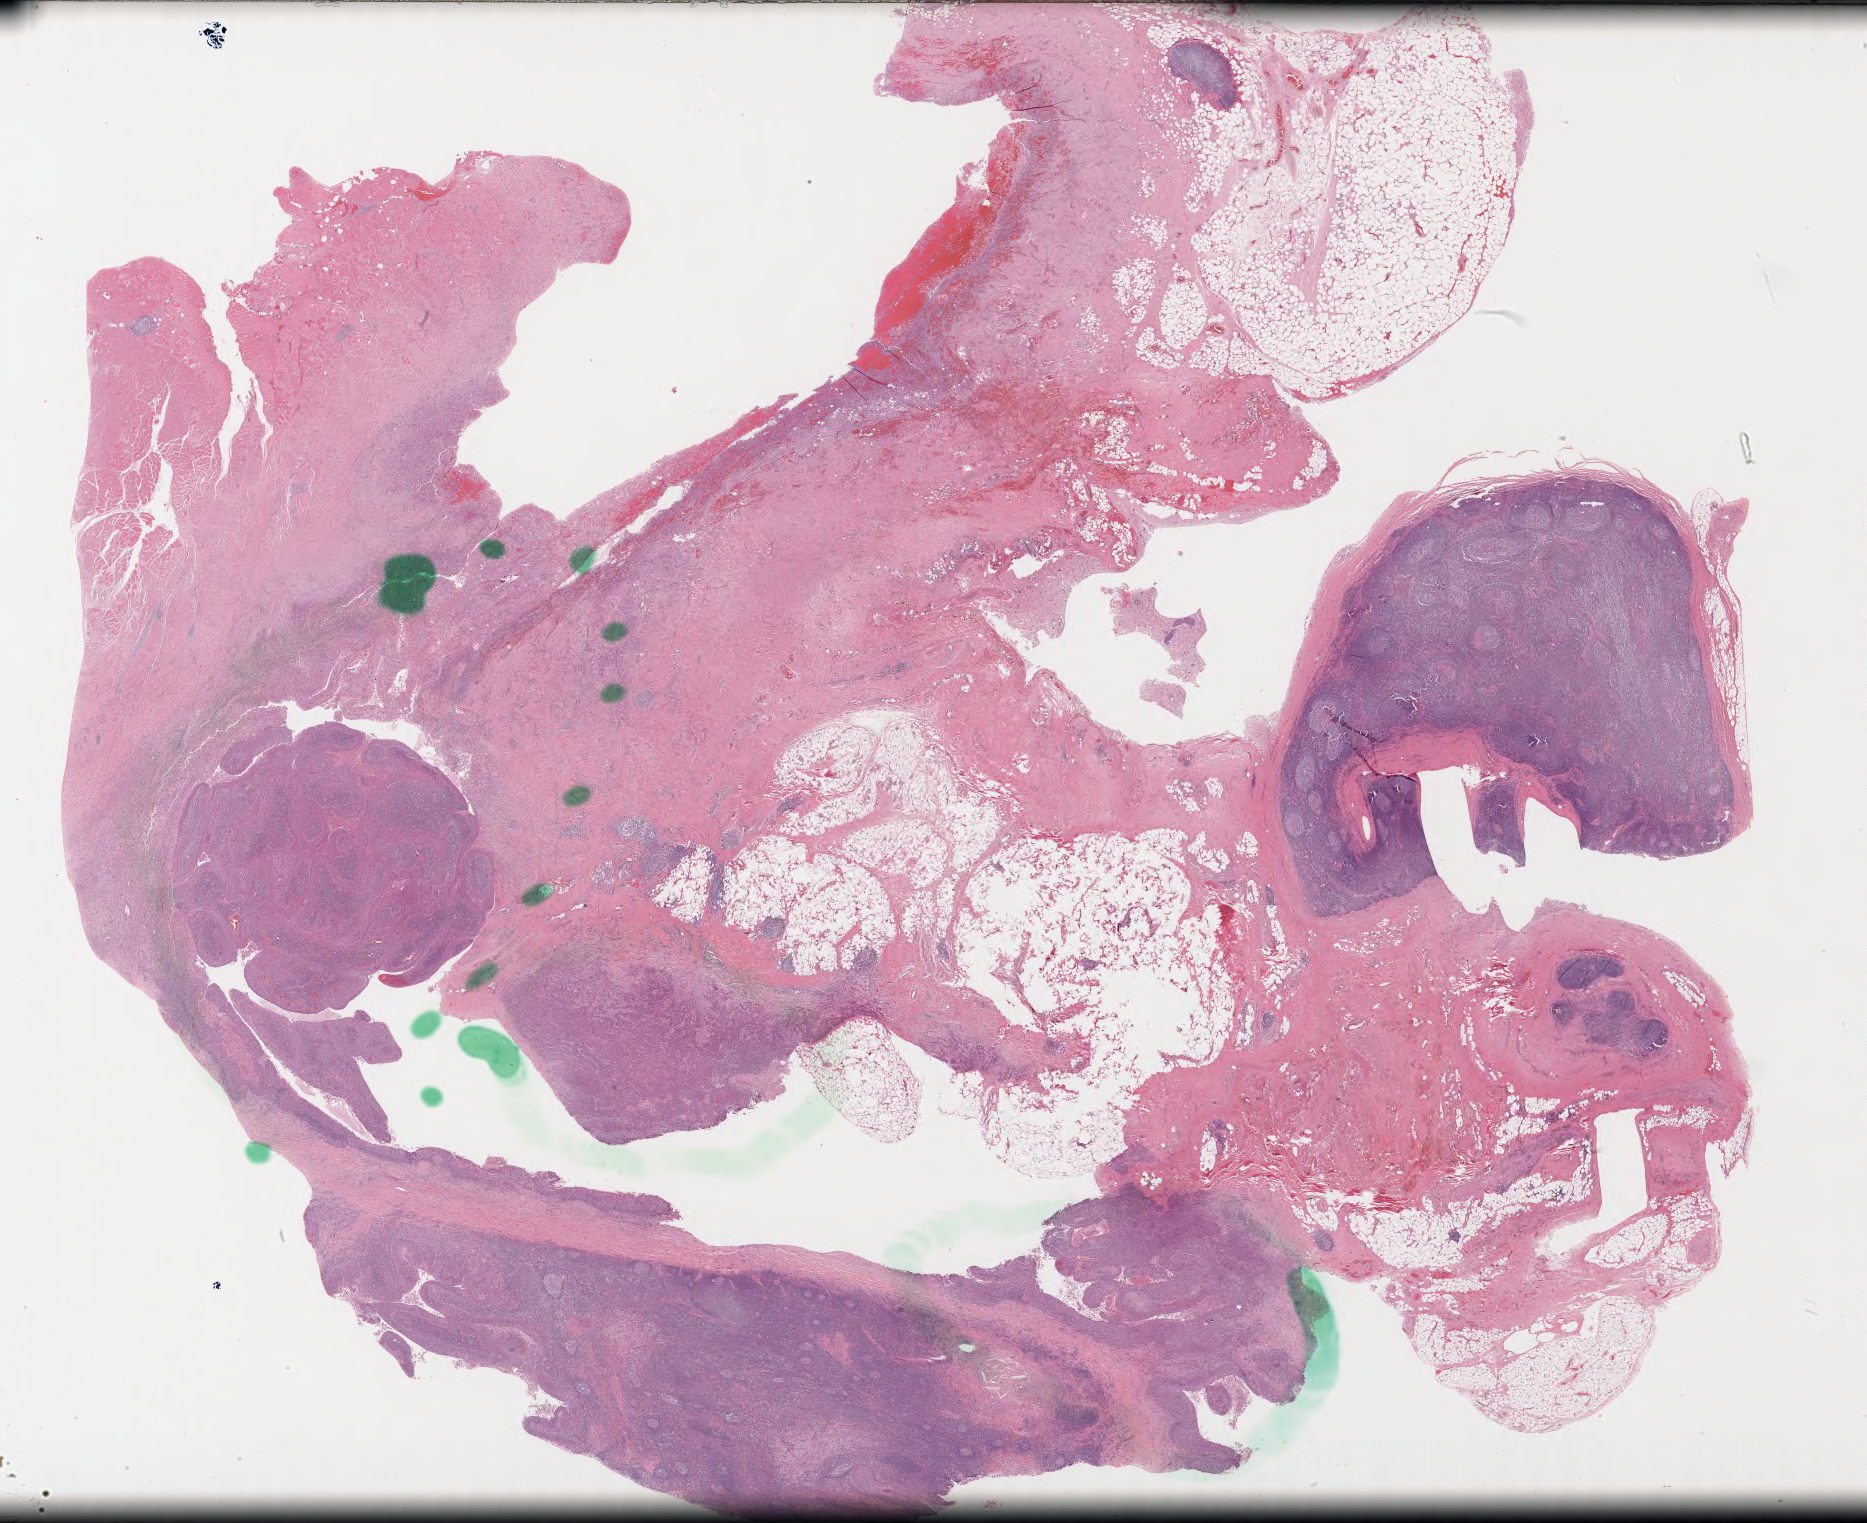
Hematoxylin and eosin (H&E) stained whole-slide image — whole scanned area (about 29.4 x 24.0 mm, from a 40x scan) shown as a low-resolution overview; formalin-fixed paraffin-embedded (FFPE) diagnostic section; head and neck, primary tumour sample. Patient: male, age at initial diagnosis 50 years. Histologic grade: G3 (poorly differentiated).
- AJCC pathologic stage: IVB (6th edition)
- histologic diagnosis: Squamous cell carcinoma, NOS (tonsil, NOS)
- laterality: left